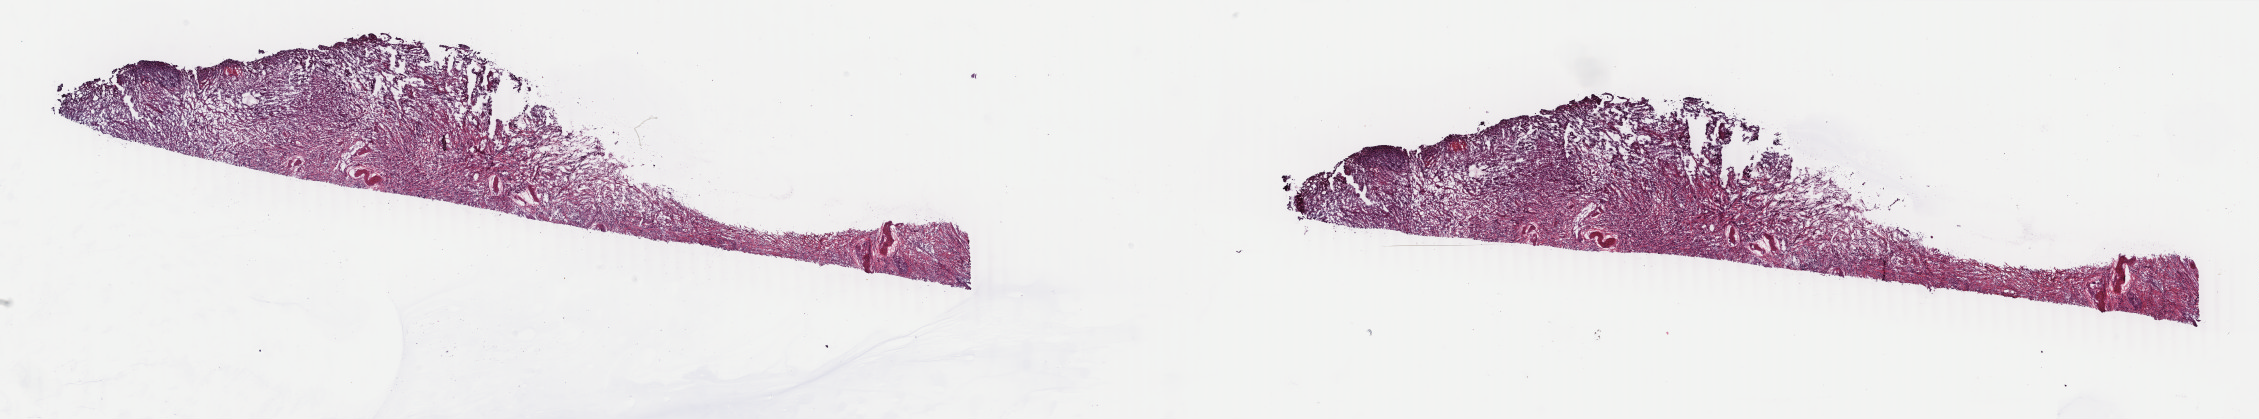
H&E whole-slide image — whole scanned area (about 35.9 x 6.7 mm, acquisition: 40x scan) shown as a low-resolution overview; frozen section from the top of the tissue portion; sample: primary tumour, stomach. Male patient; age at initial diagnosis 65 years. Histologic grade: G3 (poorly differentiated). Pathologist review of this section (percent, as recorded): tumour cells 100%, tumour nuclei 65%, normal cells 0%, stromal cells 0%, necrosis 0%. Infiltration values recorded for this section: lymphocyte infiltration 3%, monocyte infiltration 0%, neutrophil infiltration 0%.
AJCC pathologic stage: IIIA (7th edition). Histologic diagnosis: Adenocarcinoma, NOS (cardia, NOS). Lymph nodes positive (case pathology): 6 of 6 examined.